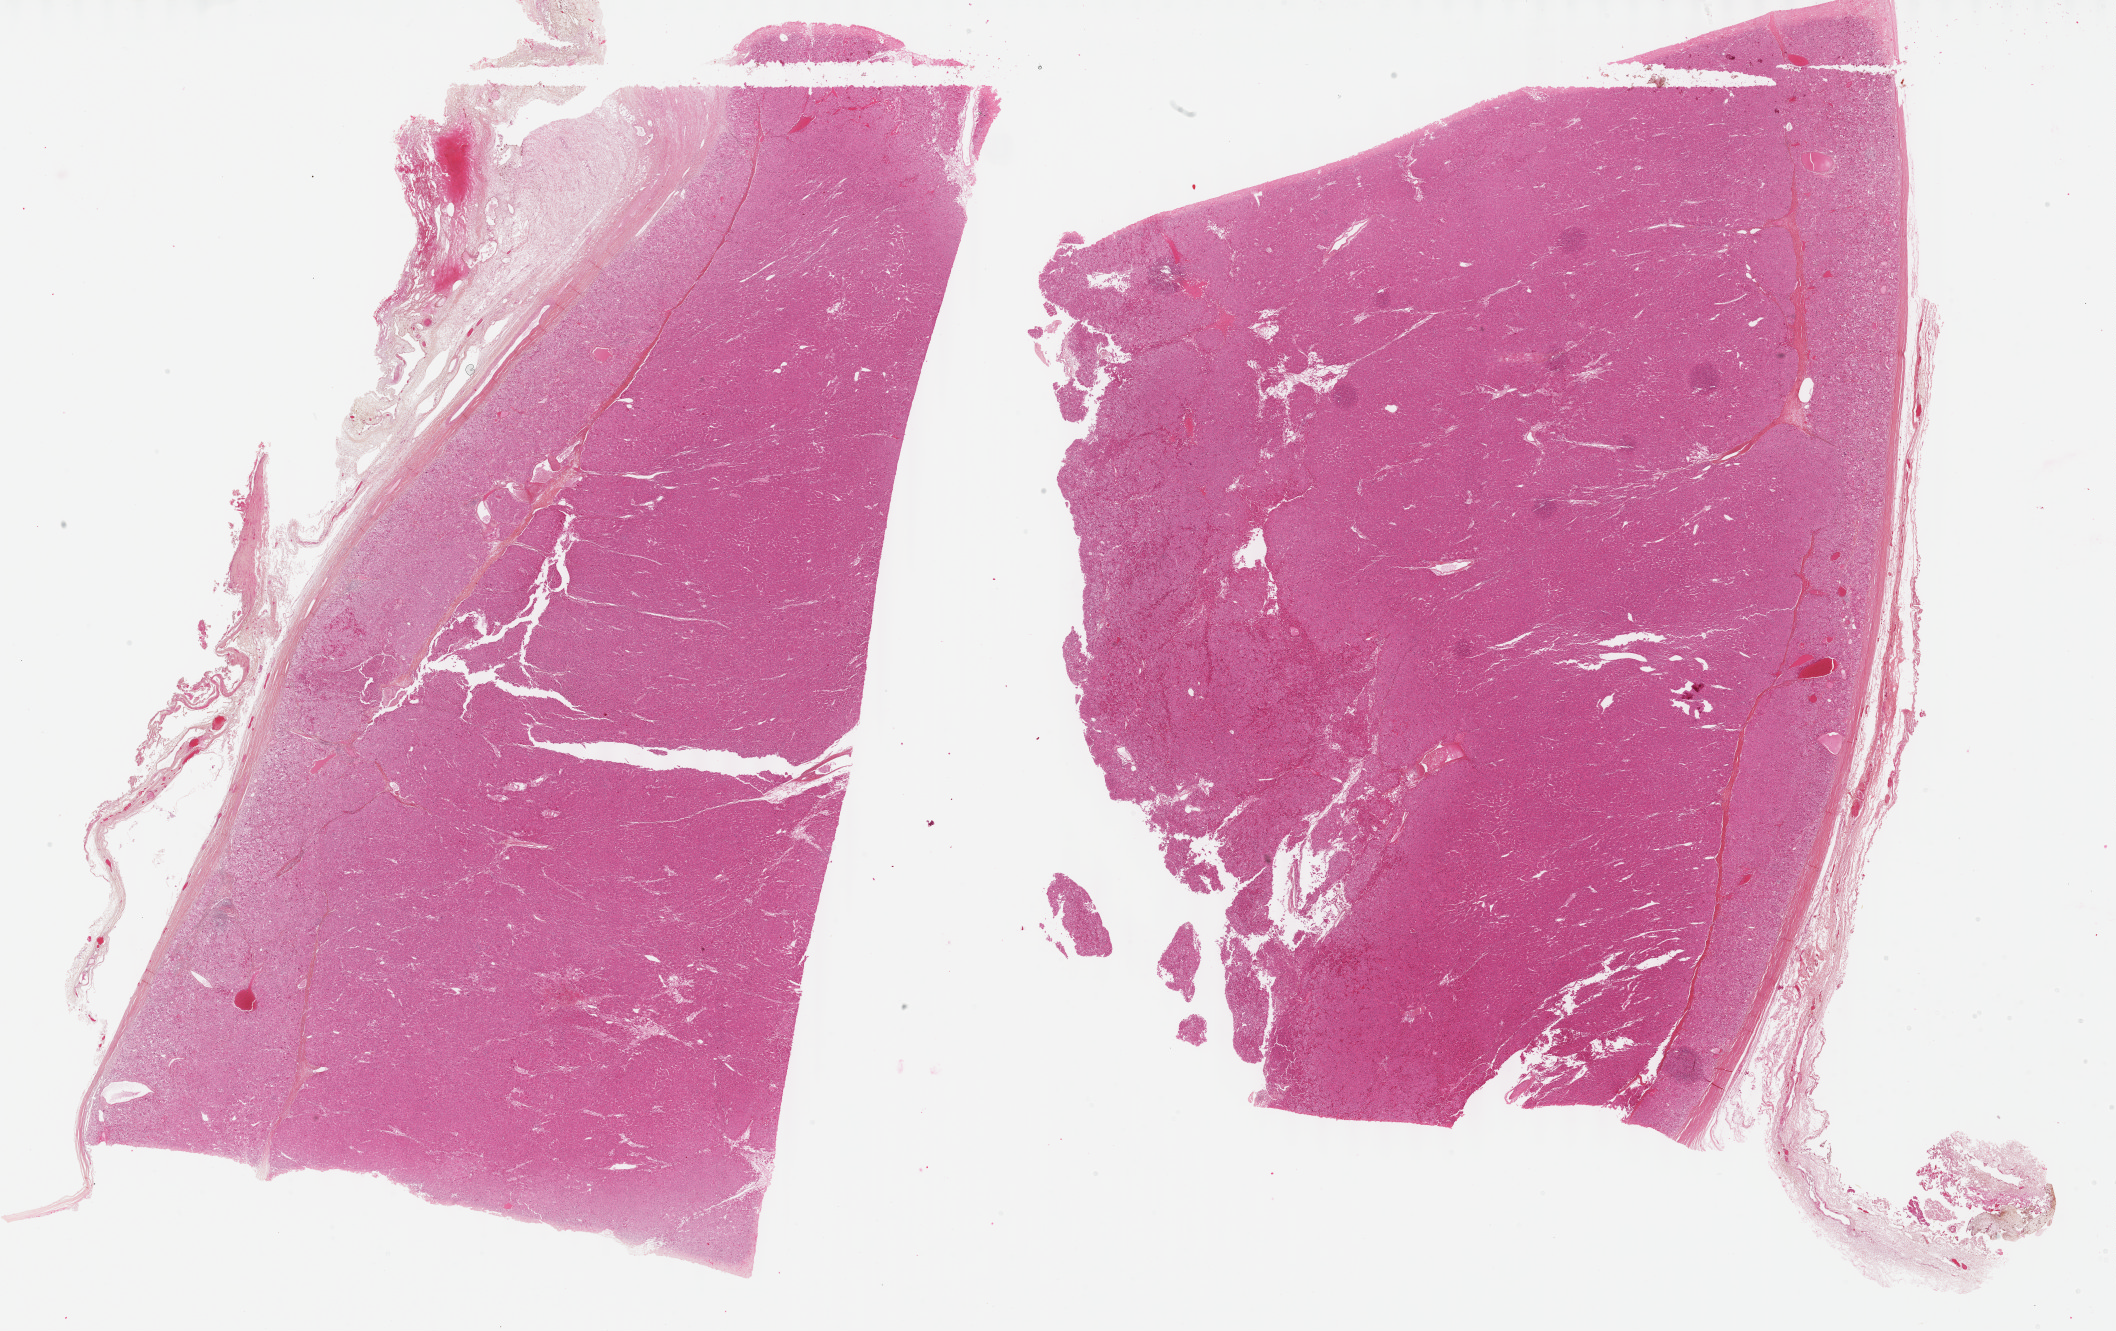
Digitized H&E-stained tissue section (whole slide) — a low-resolution overview of the entire scanned area, about 34.2 x 21.5 mm (from a 40x scan). Formalin-fixed paraffin-embedded (FFPE) diagnostic section. Primary tumour sample from the adrenal cortex. Female, age 31 years at initial diagnosis.
• lymph nodes positive (case pathology): 0 of 10 examined
• pathologic diagnosis: Adrenal cortical carcinoma (cortex of adrenal gland)